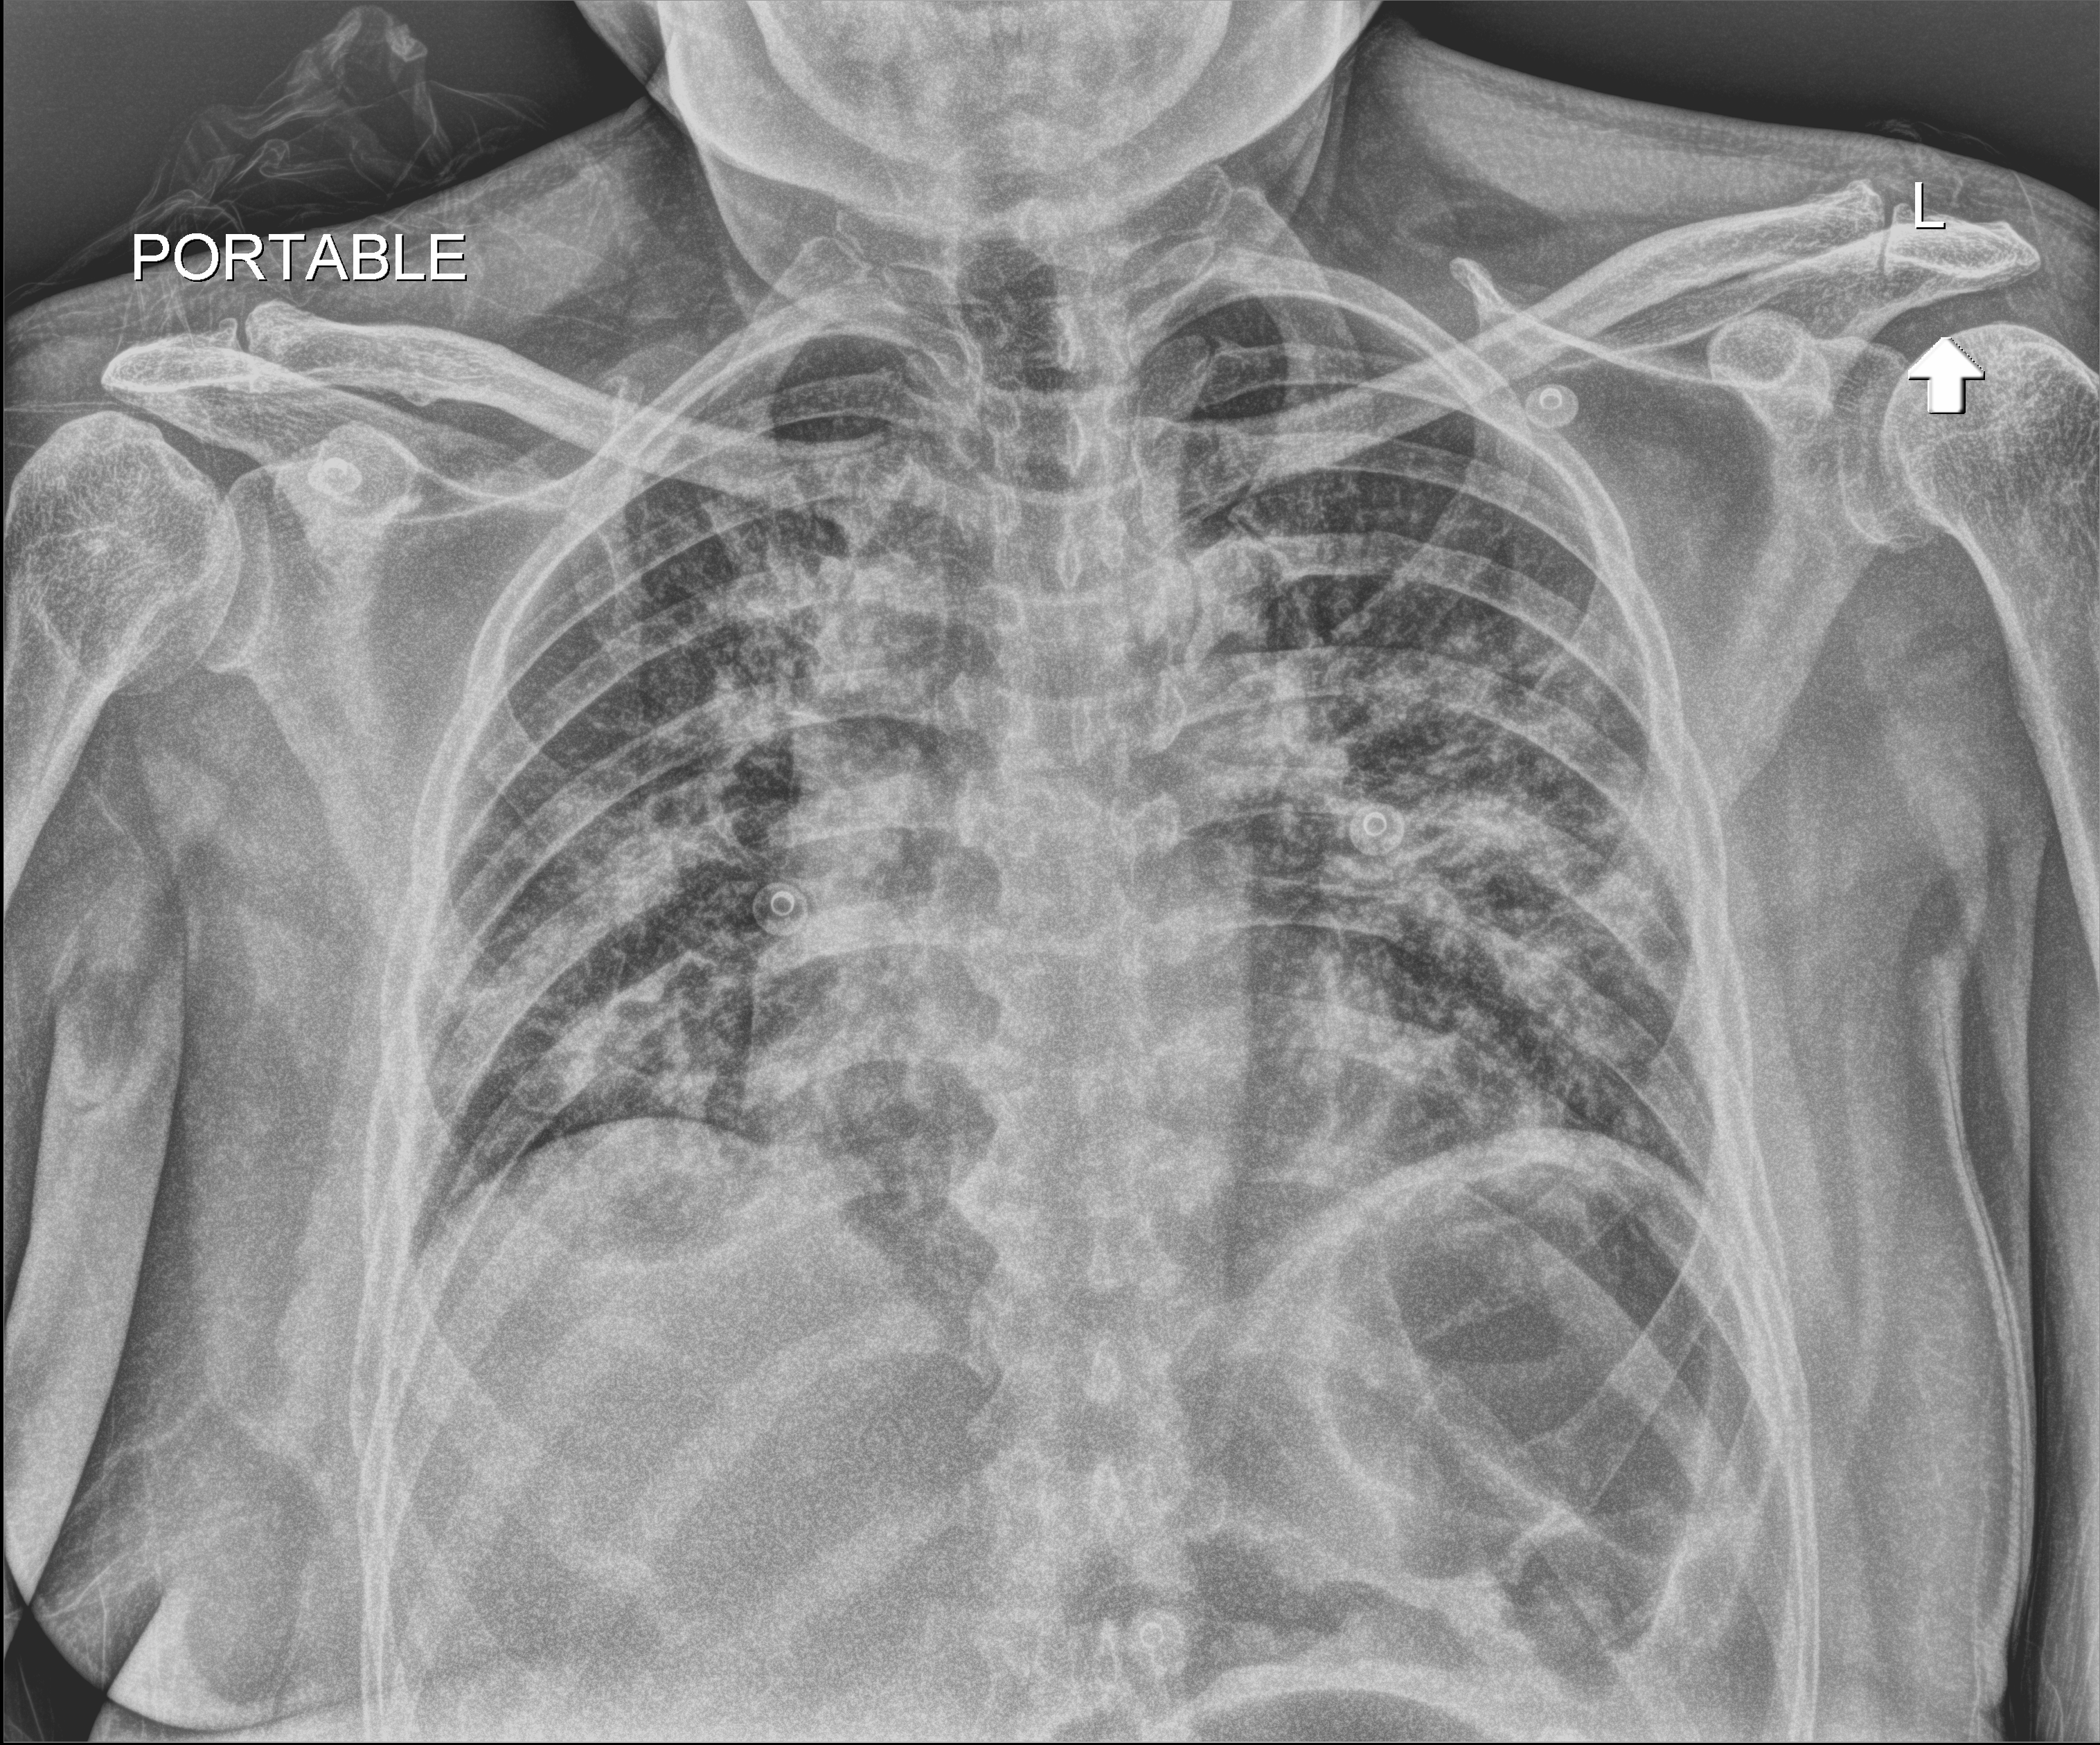
Chest X-ray. Male patient hospitalised with COVID-19, age 18–59 years.
From the hospital-stay record, not from the radiograph (when in the stay this image was taken is not recorded): length of hospital stay: 11 days; smoking status (admission record): never.